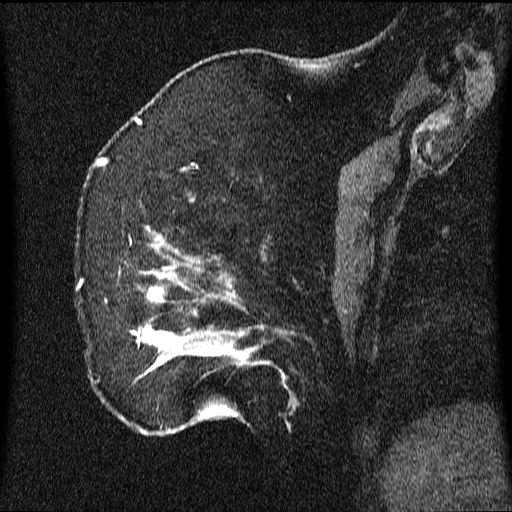
Breast MRI (dynamic contrast-enhanced), one sagittal slice. Slice 16 of 64 in the series (ordered by position). Dynamic contrast-enhanced series, image 2 of 3 at this slice position (ordered by acquisition). 1.5 T. TE 4.2 ms, TR 9.1 ms. 2.2 mm slice thickness. 512 × 512 image matrix, field of view 180 × 180 mm. Patient: female, 52 years.
Annotated regions visible in this slice (semi-automatically segmented with operator editing):
- analysis volume of interest (the breast-tissue region the enhancement analysis was run in; not a lesion): bounding box [x1, y1, x2, y2] px = [77, 204, 350, 436]
- tumour enhancement mask (voxels above the 70 % enhancement threshold inside the analysis volume of interest): [106, 227, 287, 435]